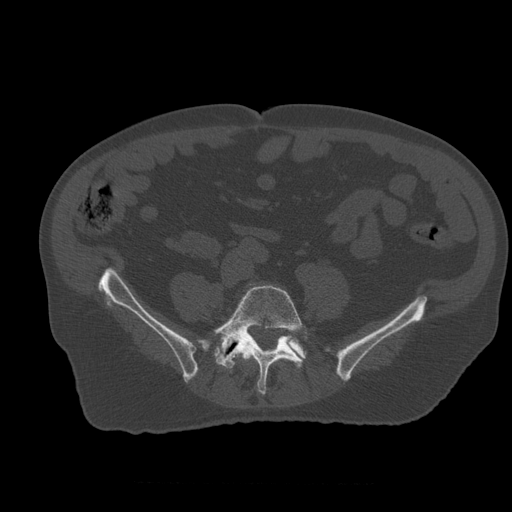
CT including the spine, one axial slice; slice 142 of 399 in the series (ordered by position); 120 kVp; bone window (W 1800 / L 400 HU); 1.25 mm slice thickness; 512 × 512 image matrix, field of view 407 × 407 mm. Patient age 73 years. From the clinical record (not read from this slice): primary cancer: prostate.
Outlined on this slice (semi-automatically segmented with operator editing):
- L4 vertebra: bounding box [x1, y1, x2, y2] px = [241, 351, 256, 361]
- L5 vertebra: [213, 284, 307, 395]